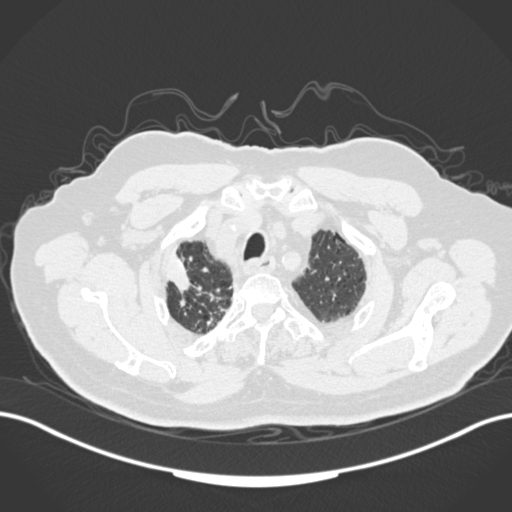
Chest CT, one axial slice. Position 149 of 205 along the scan axis. 120 kVp. Lung window (W 1500 / L -600 HU). 1 mm slice thickness. 512 × 512 image matrix, field of view 400 × 400 mm. Male patient, age 72 years. From the clinical record (not read from this slice): clinical TNM (as recorded): T1a N0 M0.
Structures marked on this image (bounding box drawn by a radiologist):
- lung tumour (recorded histology: squamous cell carcinoma): bounding box (x1, y1, x2, y2) in pixels: (158, 242, 201, 307)